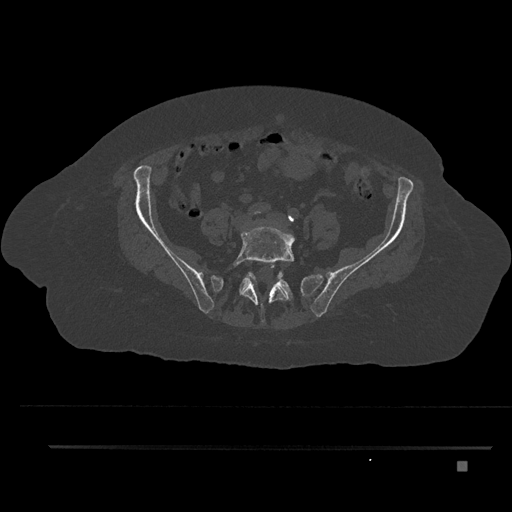
CT including the spine, one axial slice; position 33 of 797 along the scan axis; reconstruction kernel Br40s/3; bone window (W 1800 / L 400 HU); 0.5 mm slice thickness; 512 × 512 image matrix, field of view 437 × 437 mm. Patient: female, 76 years. Case-level facts recorded for this patient, not image findings: primary cancer: lung; vertebrae with lytic lesions (as recorded): T11, L3.
Structures marked on this image (semi-automatically segmented with operator editing):
- L5 vertebra: bounding box [x1, y1, x2, y2] px = [233, 224, 296, 324]